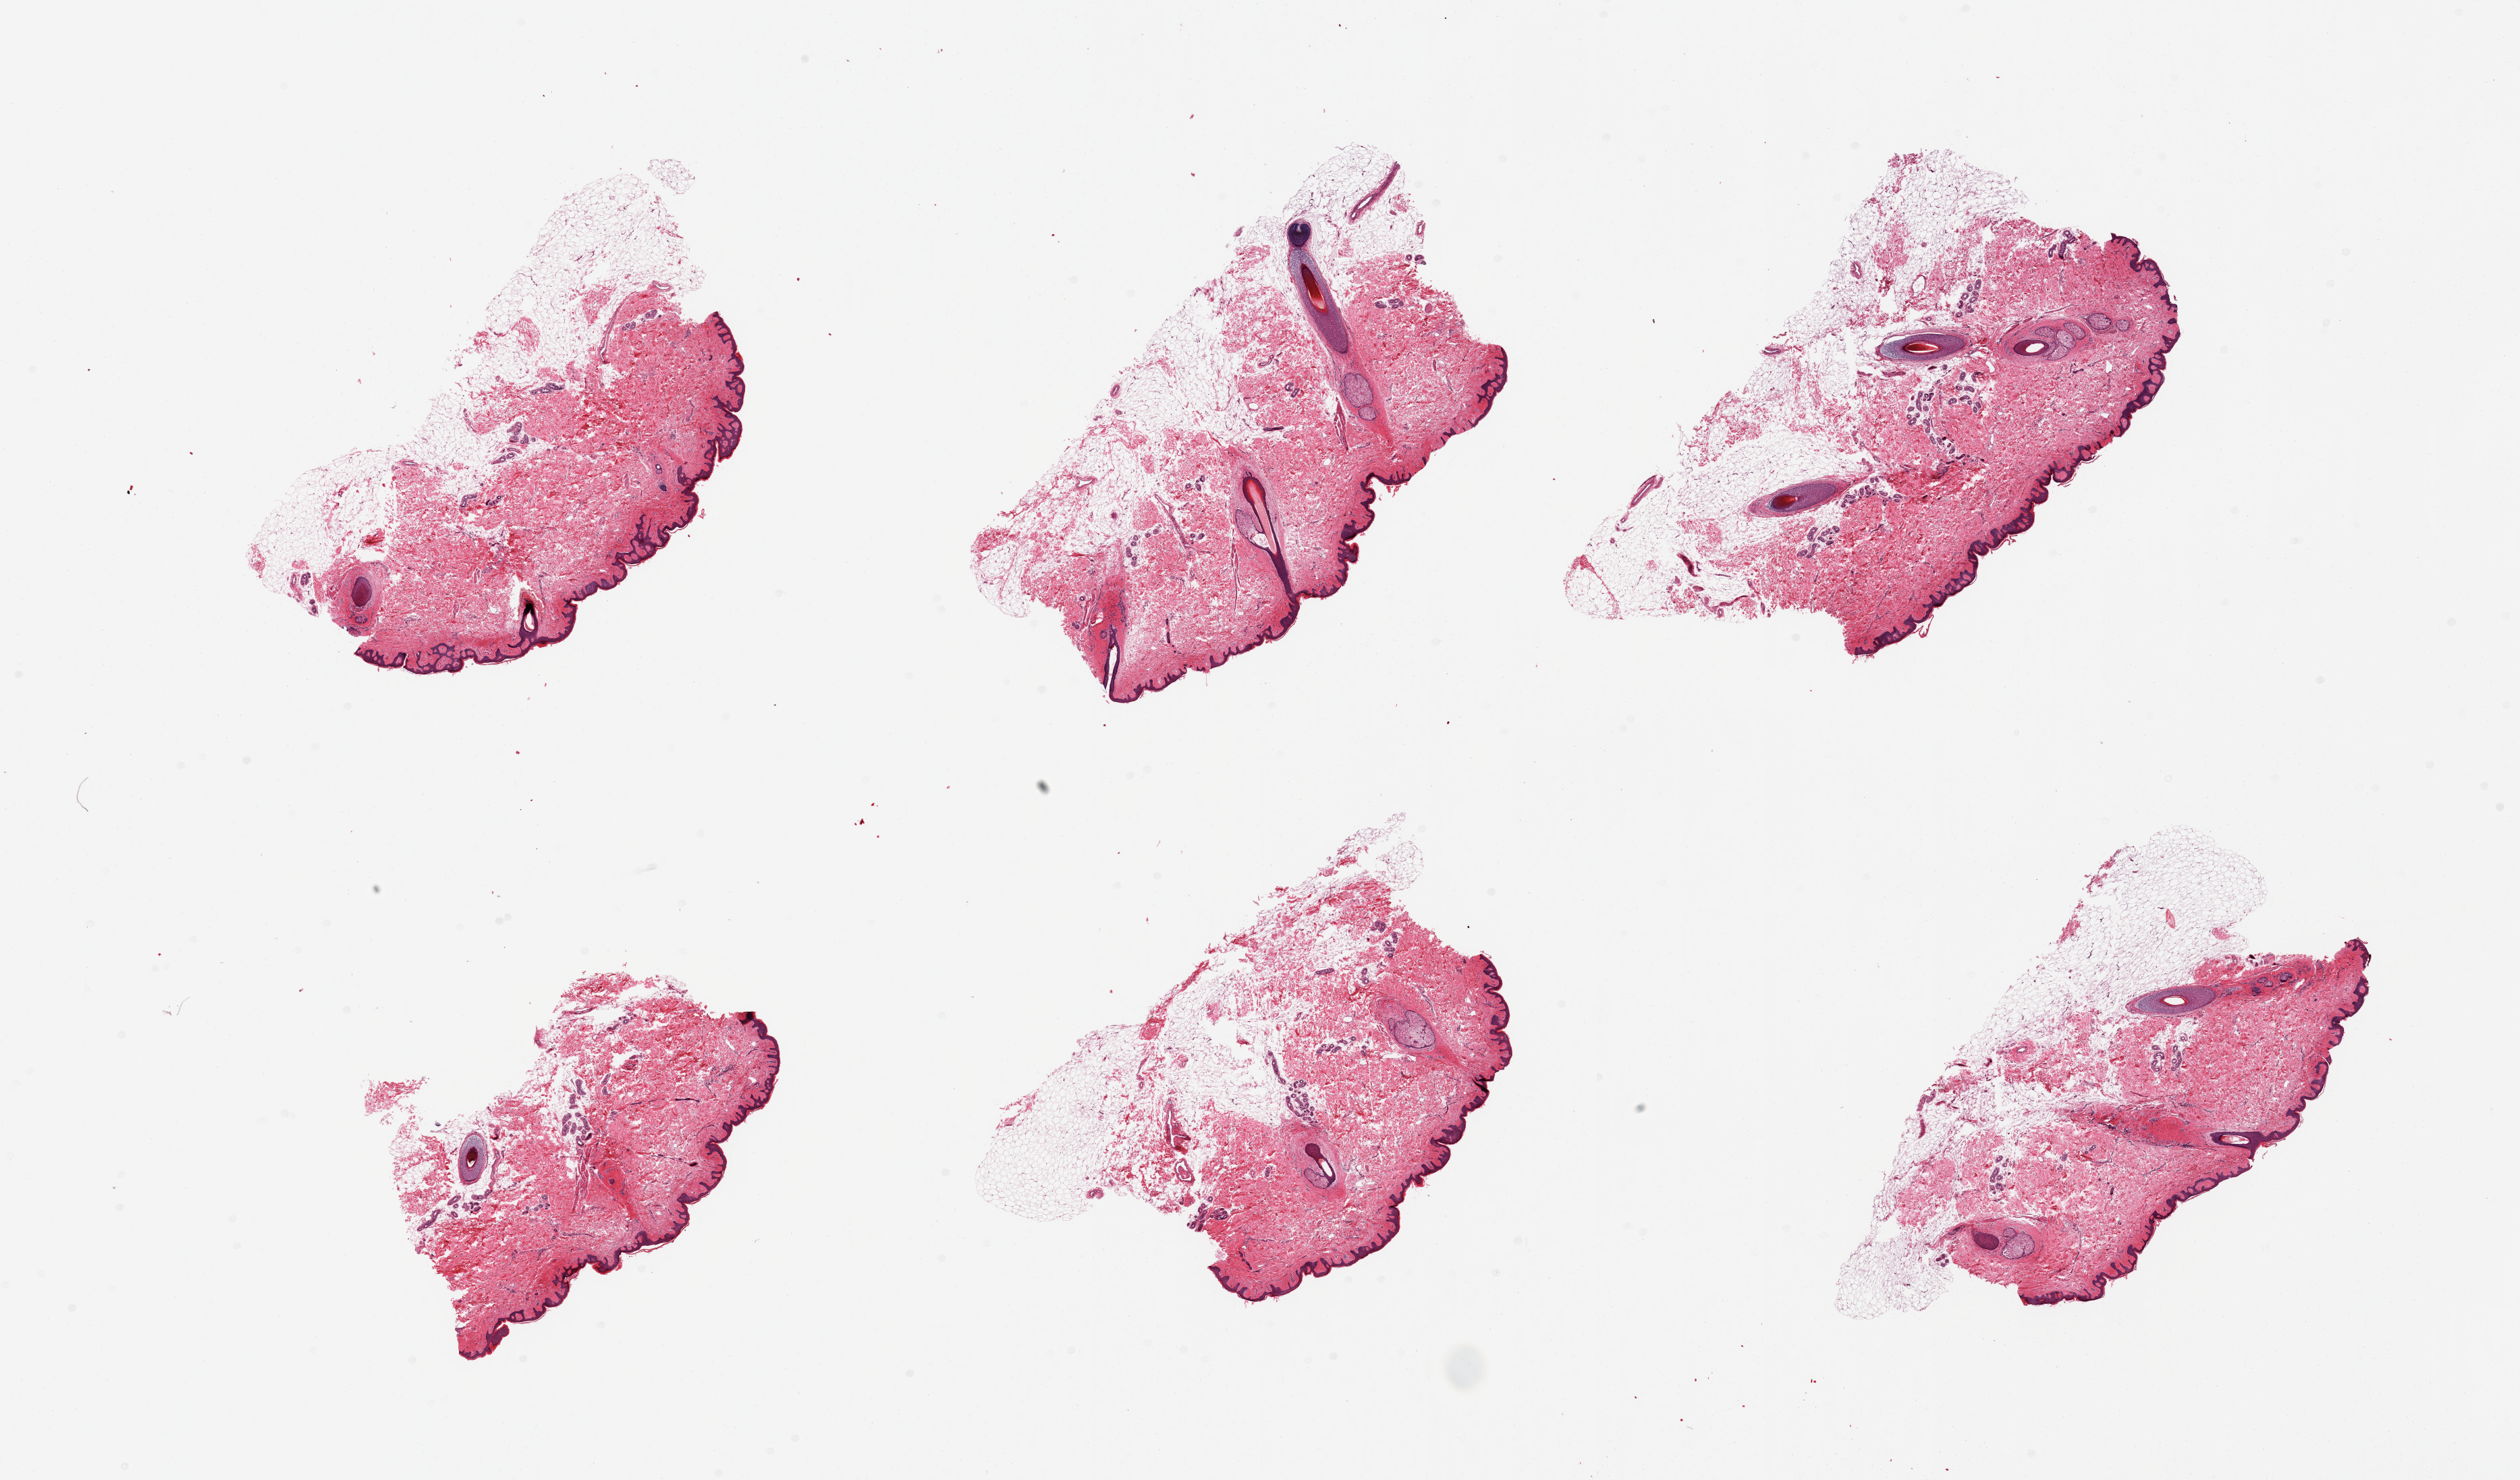
Digitized H&E-stained section — a low-resolution overview of the entire scanned area, about 29.5 x 17.3 mm; PAXgene-fixed, paraffin-embedded tissue; target tissue: skin of suprapubic region; tissue donor sample.
Pathologist's review note for this sample: 6 pieces; hair-bearing skin, several include significant attached fat, up to 50%.